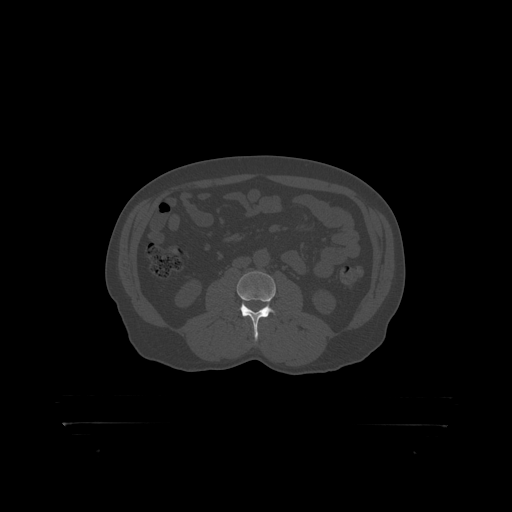
CT including the spine, one axial slice. Slice 264 of 399 in the series (ordered by position). Reconstruction kernel STANDARD. Bone window (W 1800 / L 400 HU). 1.25 mm slice thickness. 512 × 512 image matrix, field of view 650 × 650 mm. Male patient, age 46 years. From the clinical record (not read from this slice): primary cancer: skin.
Structures marked on this image (semi-automatic segmentation, software-assisted and operator-edited):
- L3 vertebra: box from (x=237, y=272) to (x=277, y=319) px